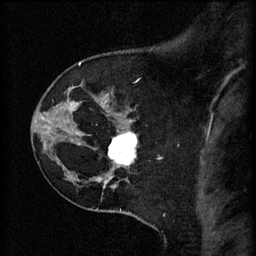
Breast MRI (dynamic contrast-enhanced), one sagittal slice. Slice 46 of 60 in the series (ordered by position). 3 images stored at this slice position (order not interpretable as contrast timing). 1.5 T. TE 4.2 ms, TR 11 ms. 256 × 256 image matrix, field of view 180 × 180 mm. Patient: female, 45 years.
Annotated regions visible in this slice (semi-automatically segmented with operator editing):
- analysis volume of interest (the breast-tissue region the enhancement analysis was run in; not a lesion): bounding box [x1, y1, x2, y2] px = [110, 128, 139, 171]
- tumour enhancement mask (voxels above the 70 % enhancement threshold inside the analysis volume of interest): [110, 132, 137, 165]